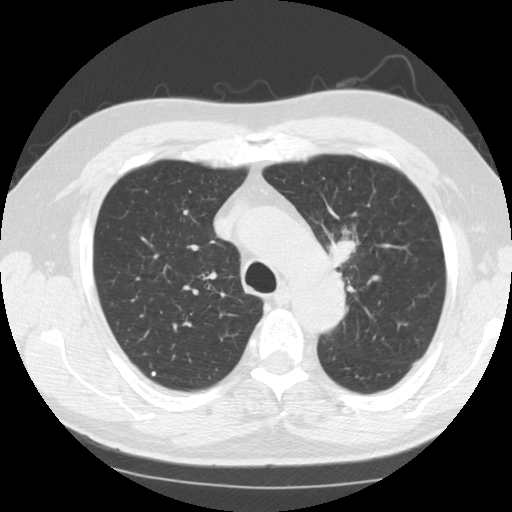
Chest CT (low-dose screening protocol), one axial image. Third annual screen. Lung window (W 1500 / L -600 HU). Standard (soft-tissue) reconstruction kernel (STANDARD). Slice 31 of 124 in the series. 512 × 512 image matrix, field of view 340 × 340 mm. Male participant, aged 60 years at enrolment.
Lesion marked by an expert reader, bounding box [x1, y1, x2, y2] px = [318, 228, 371, 289]. The exam's reader record, not a measurement of the box and not confirmed to be the same lesion: non-calcified nodule or mass ≥4 mm, left upper lobe, 24 × 21 mm, smooth margins, soft tissue attenuation, pre-existing on the prior screen: no. Later outcome: lung cancer diagnosed 14 days after this screen — small cell carcinoma, NOS, left upper lobe, stage IIA (AJCC 6th edition), 26 mm at pathology.